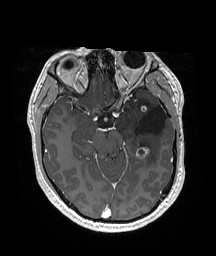
Brain MRI from a brain-tumour surgery series, one axial slice; slice 109 of 192 in the series (ordered by position); T1-weighted post-contrast; 216 × 256 image matrix, field of view 211 × 250 mm. From the clinical record (not read from this slice): histopathology: Glioneuronal tumor; WHO grade: 2; tumour location: Left Superior Temporal Gyrus.
Annotated regions visible in this slice (expert manual segmentation):
- previous resection cavity: box from (x=135, y=105) to (x=167, y=134) px
- tumour: (x=136, y=105)–(x=155, y=161)